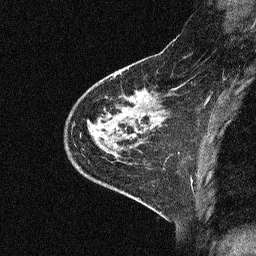
Breast MRI (dynamic contrast-enhanced), one sagittal slice. Slice 18 of 64 in the series (ordered by position). Dynamic contrast-enhanced study with each time point stored as its own series, time point 2 of 3 at this slice position (early post-contrast, ordered by acquisition time). 1.5 T. TE 4.5 ms, TR 11 ms. 256 × 256 image matrix, field of view 200 × 200 mm. Patient: female, 46 years. From the clinical record (not read from this slice): setting: breast cancer imaged before/during neoadjuvant chemotherapy; receptor status: HER2-positive.
Annotated regions visible in this slice (semi-automatic segmentation, software-assisted and operator-edited):
- analysis volume of interest (the breast-tissue region the enhancement analysis was run in; not a lesion): box from (x=46, y=51) to (x=180, y=169) px
- tumour enhancement mask (voxels above the 90 % enhancement threshold inside the analysis volume of interest): (x=104, y=110)–(x=123, y=141)